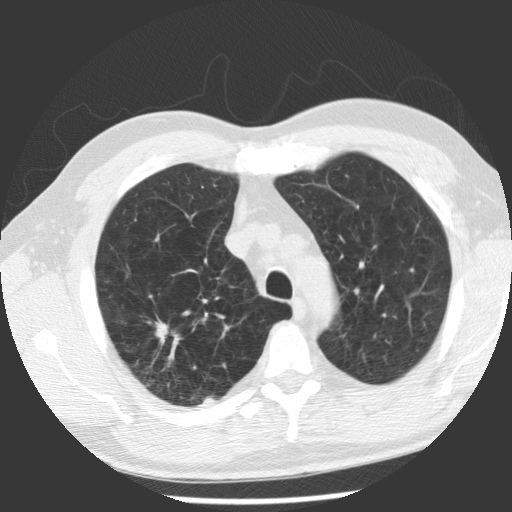
Low-dose screening chest CT, one axial slice; position 87 of 112 along the scan axis; lung window (W 1500 / L -600 HU); 512 × 512 image matrix, field of view 344 × 344 mm.
Structures marked on this image (outlined manually by an expert reader):
- lesion 1 (tumor, upper lobe of right lung): bounding box [x1, y1, x2, y2] px = [155, 322, 168, 344]